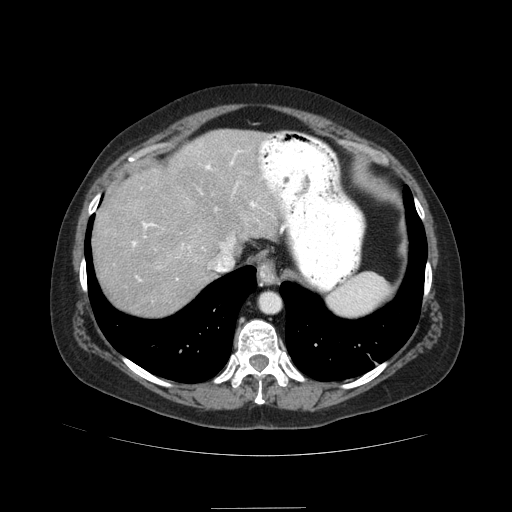
Contrast-enhanced abdominal CT (liver protocol), one axial slice. Position 71 of 89 along the scan axis. Reconstruction kernel STANDARD. 120 kVp. Soft-tissue window (W 400 / L 40 HU). 2.5 mm slice thickness. 512 × 512 image matrix. Case-level facts recorded for this patient, not image findings: diagnosis: hepatocellular carcinoma (patient treated with transarterial chemoembolisation; whether this scan precedes or follows treatment is not stated here); TNM stage (as recorded): Stage-IIIB; Child-Pugh class: A; tumour nodularity: multinodular.
Annotated regions visible in this slice (semi-automatically segmented with operator editing):
- abdominal aorta: box from (x=260, y=293) to (x=279, y=312) px
- liver parenchyma outside the tumour (the mass and vessels are separate outlines, so this box may not span the whole liver): (x=92, y=130)–(x=279, y=316)
- liver vessels: (x=132, y=151)–(x=257, y=280)